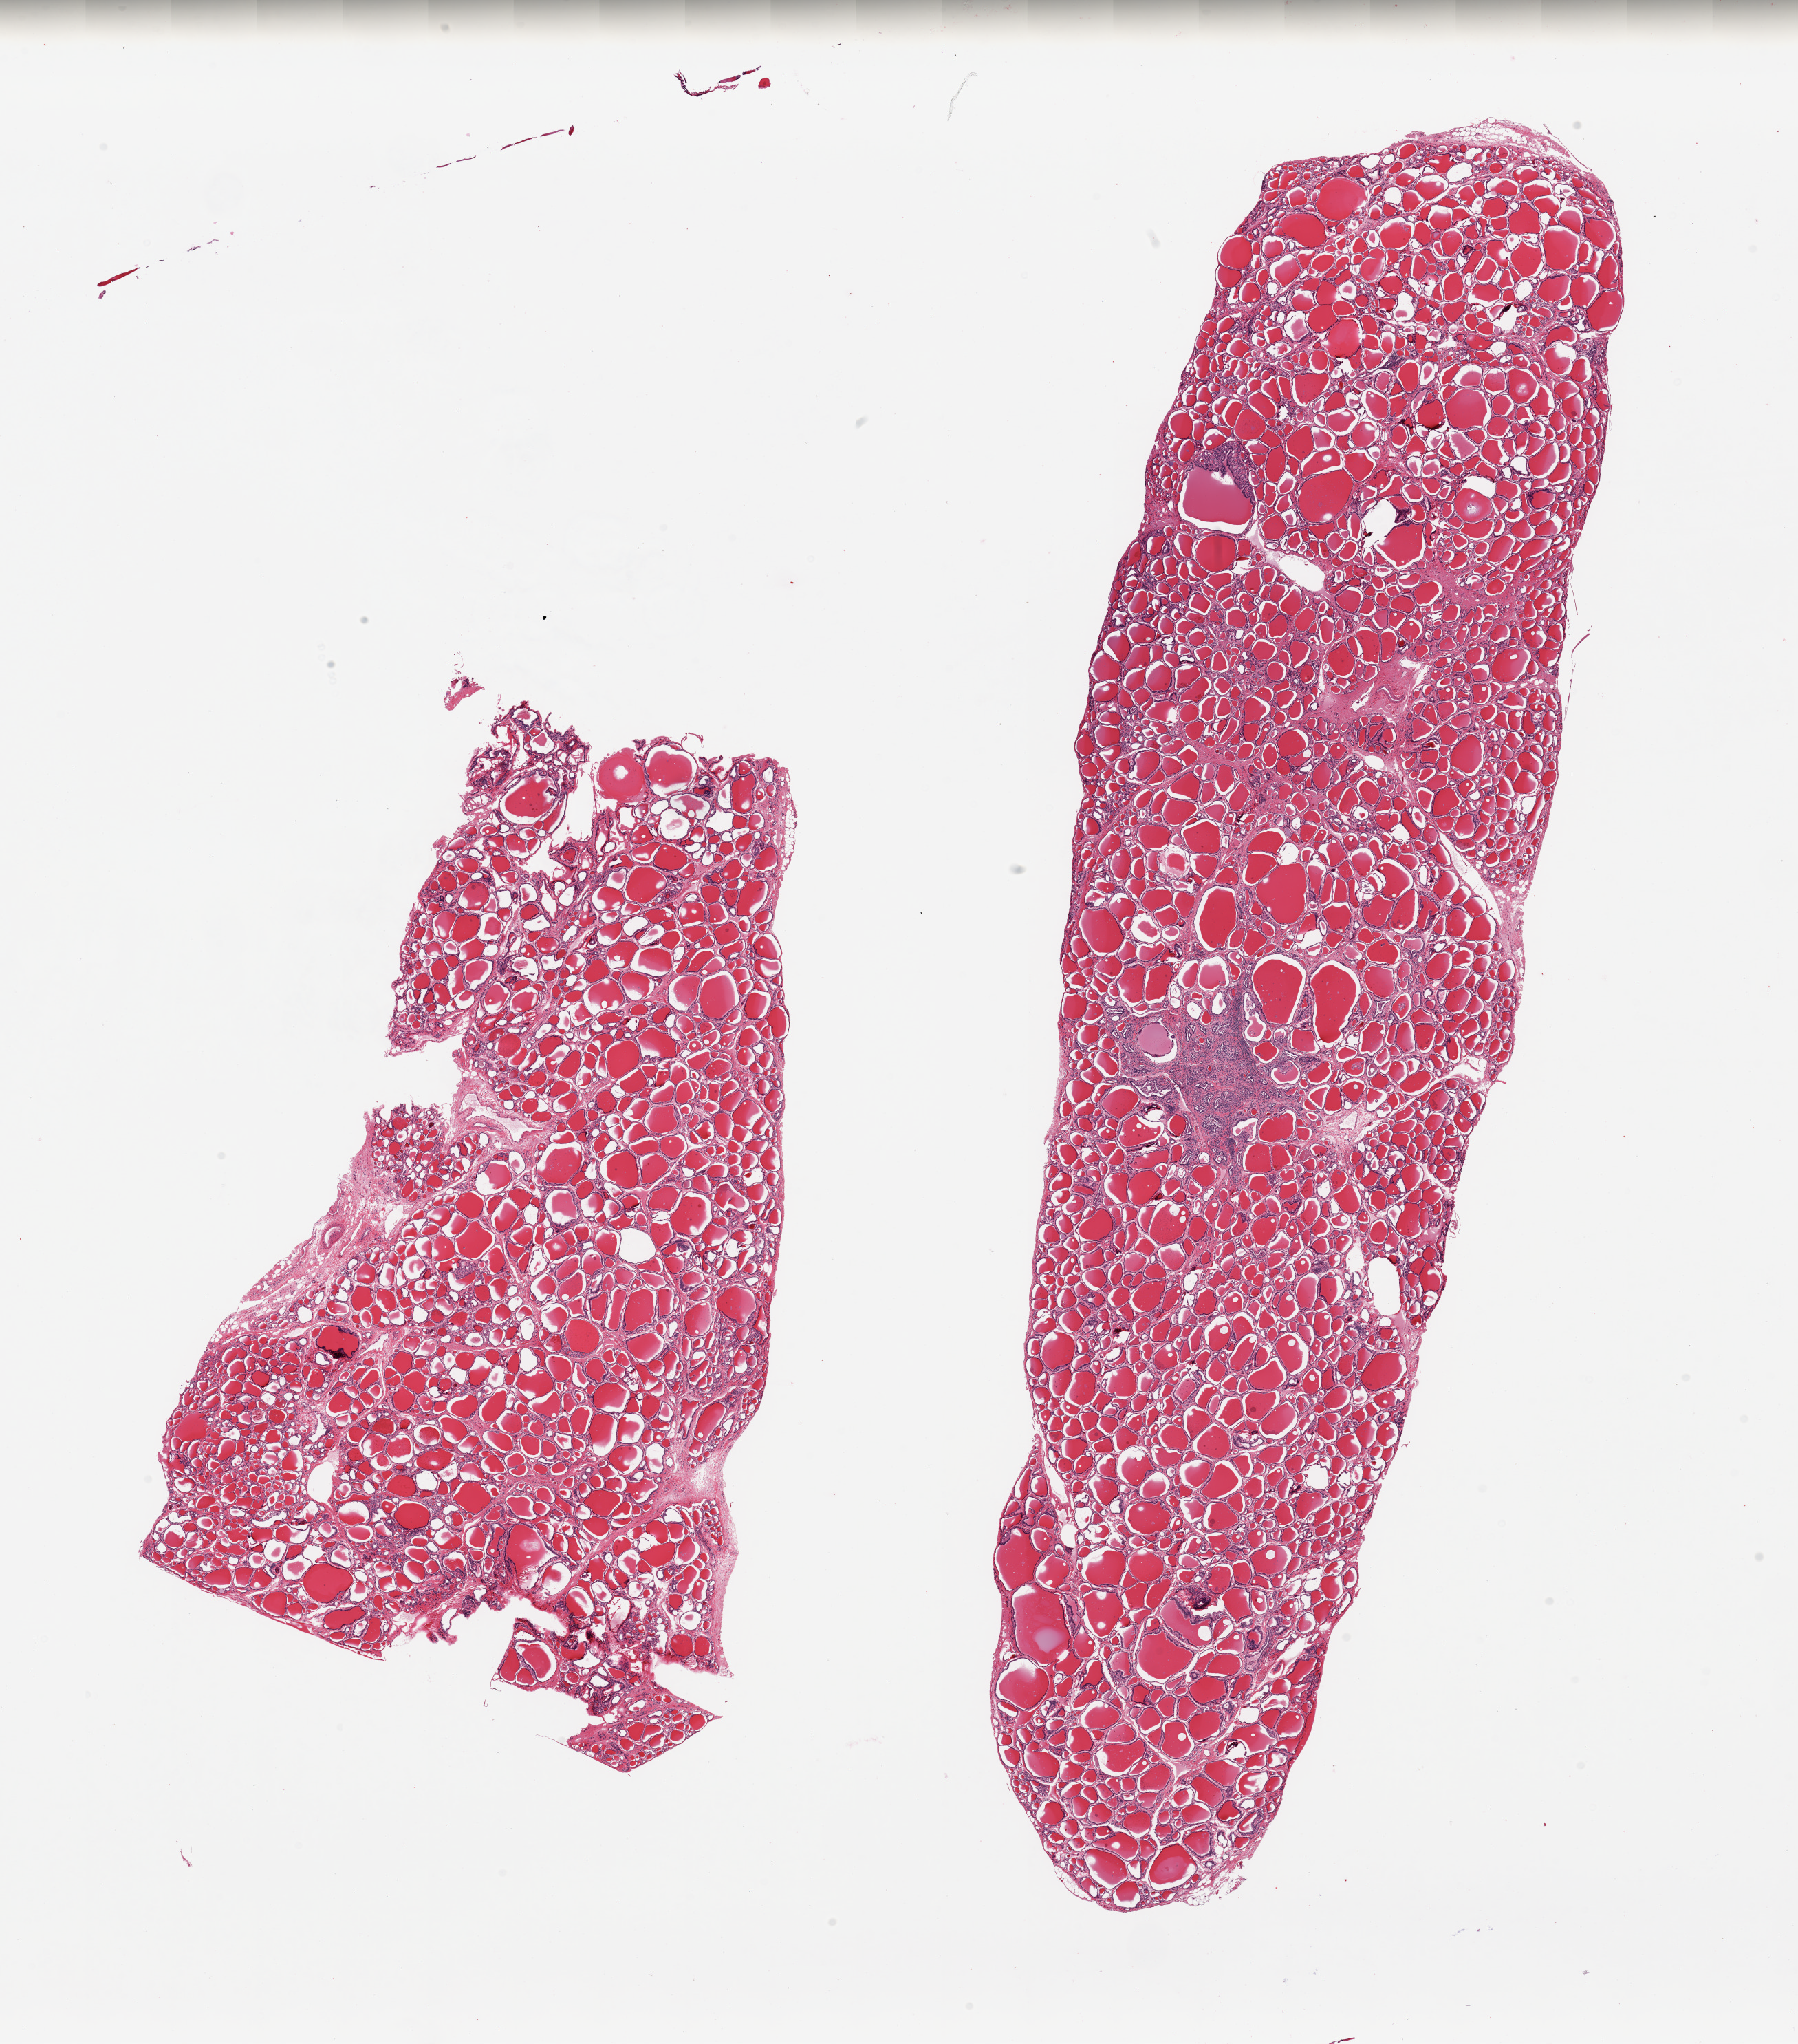
H&E whole-slide image, whole scanned area (about 20.7 x 23.5 mm) shown as a low-resolution overview, PAXgene-fixed paraffin-embedded (PFPE) section, sampled site (target tissue): thyroid, tissue donor sample. Donor: female.
Pathologist's review note for this sample: 2 pieces; focal cystic change, fibrosis, and multinucleated giant cells.